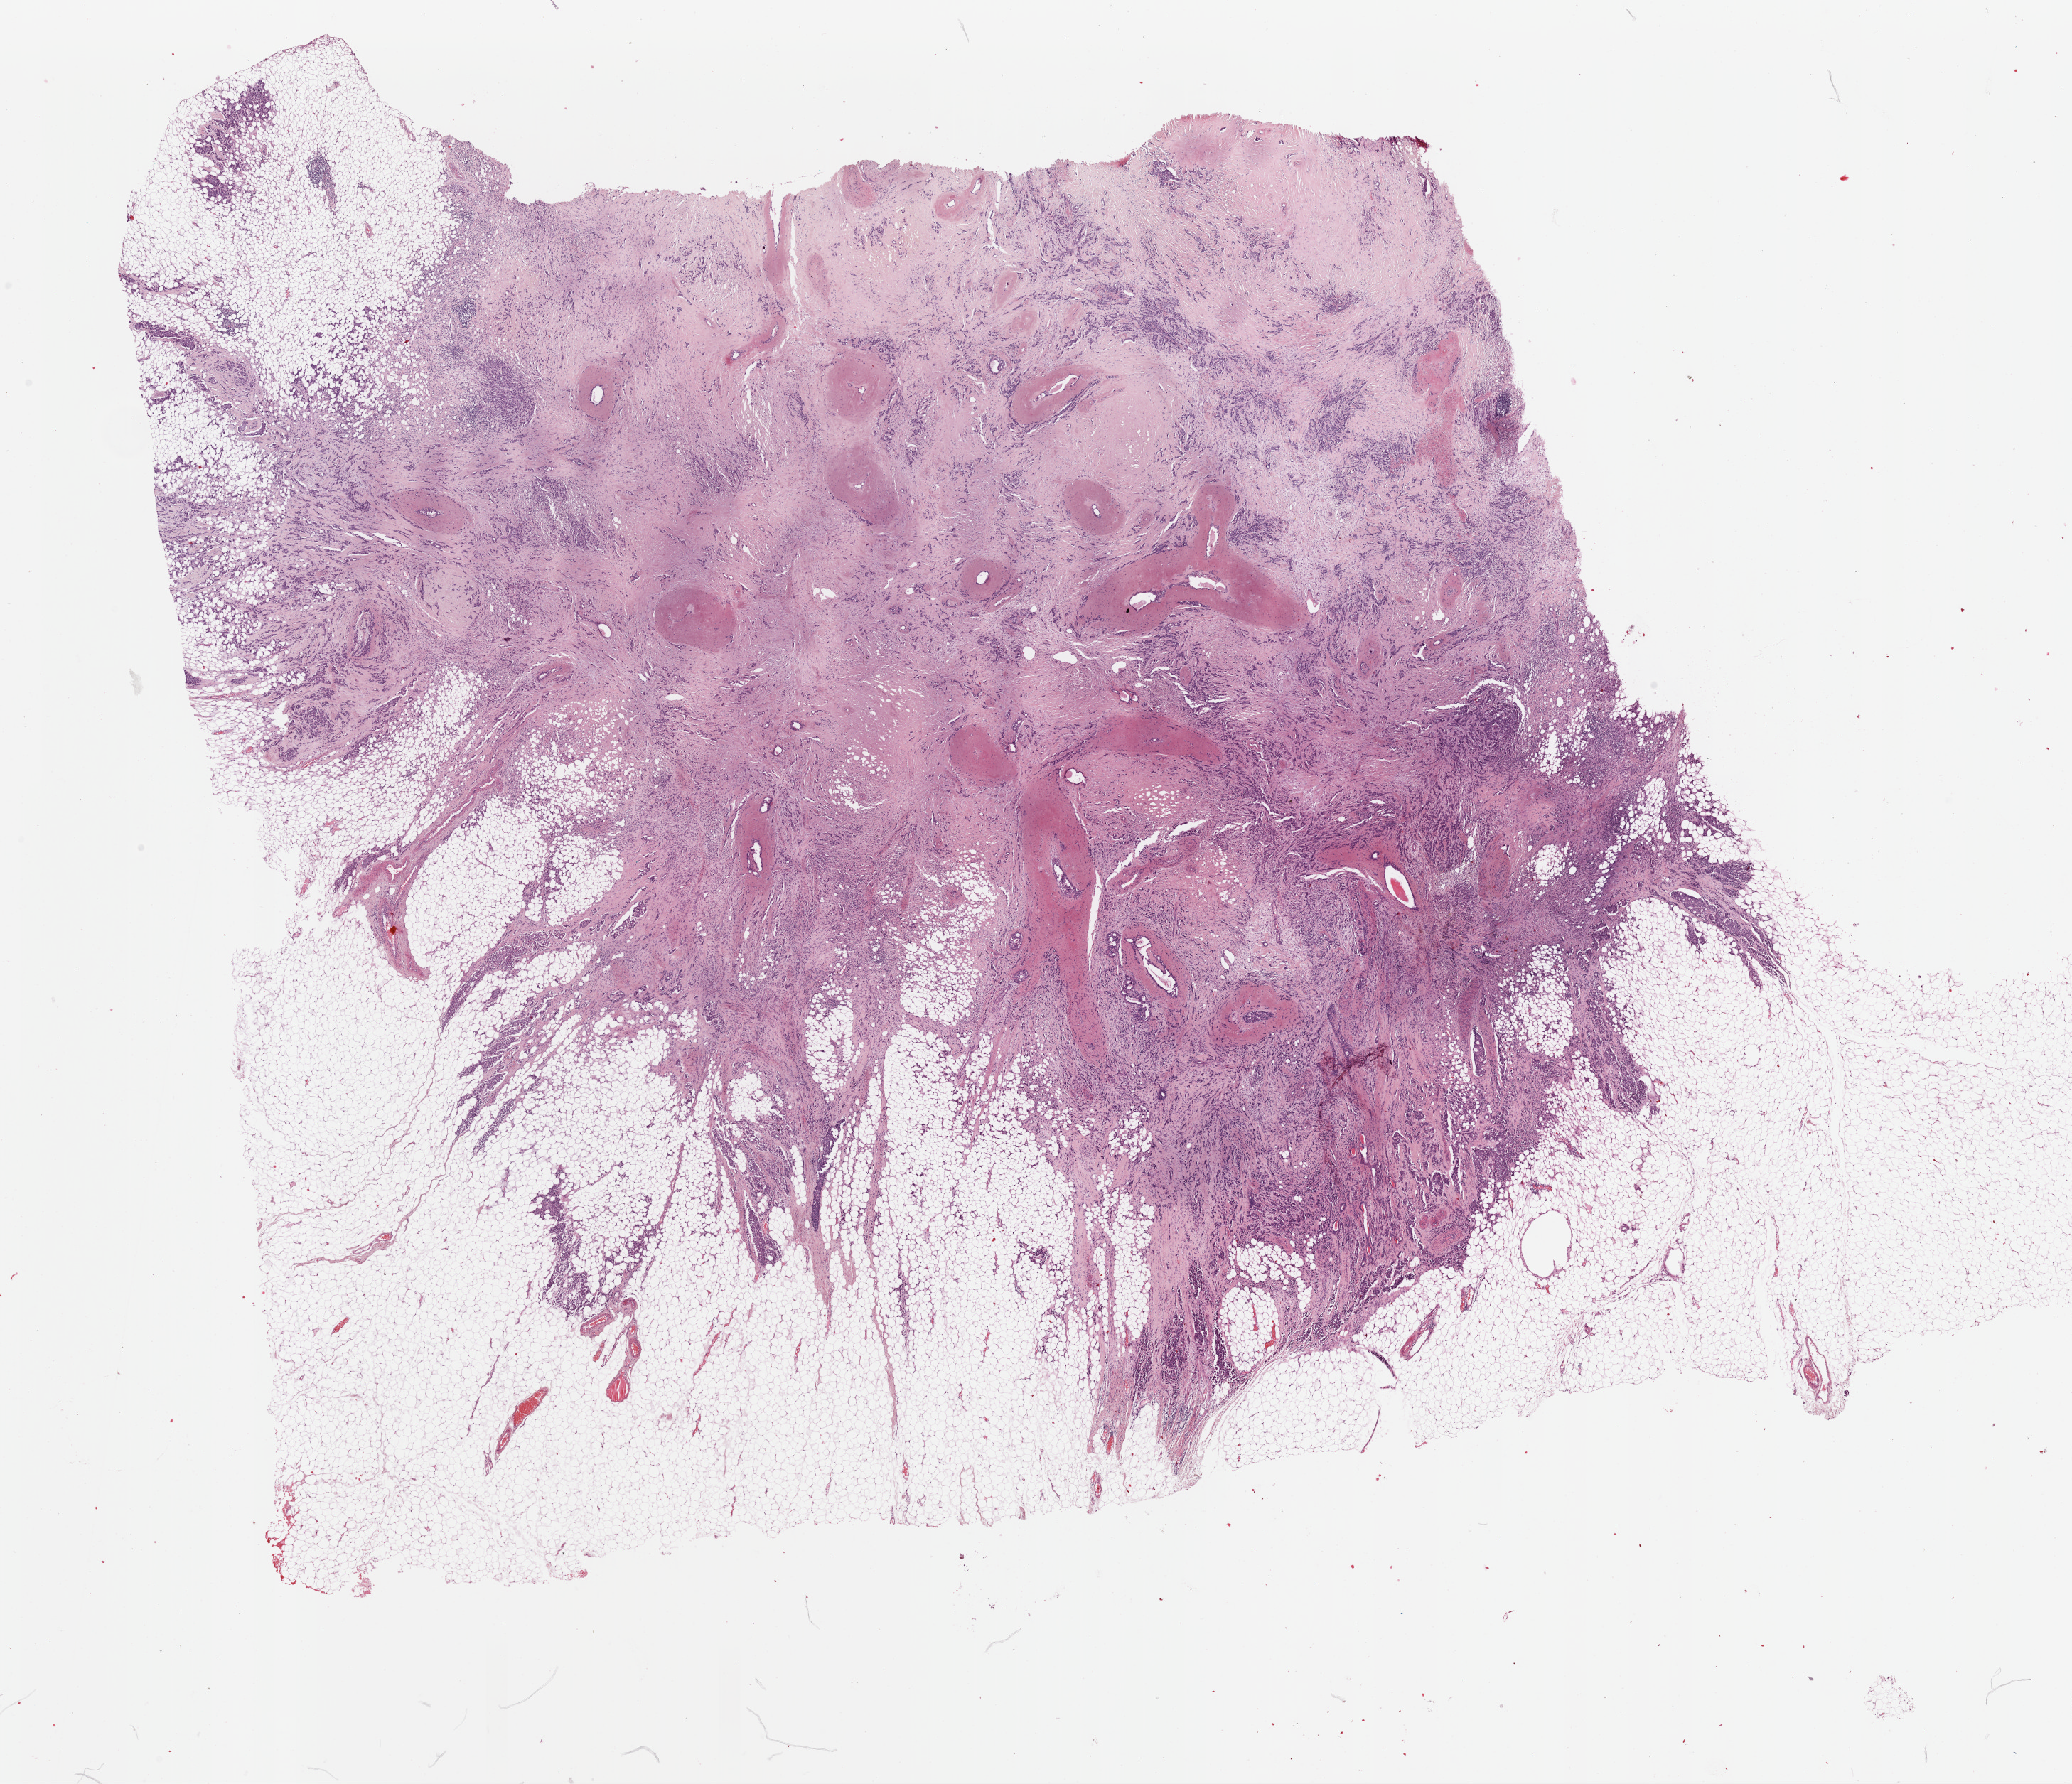
Digitized H&E tissue section (whole slide) — shown as a low-resolution overview of the whole scanned area (about 23.0 x 19.8 mm); formalin-fixed paraffin-embedded (FFPE) diagnostic section; primary tumour sample from the breast. Female patient; age at initial diagnosis 71 years.
* lymph nodes positive (case pathology): 0 of 7 examined
* AJCC pathologic stage: IIA
* diagnosis: Infiltrating duct carcinoma, NOS